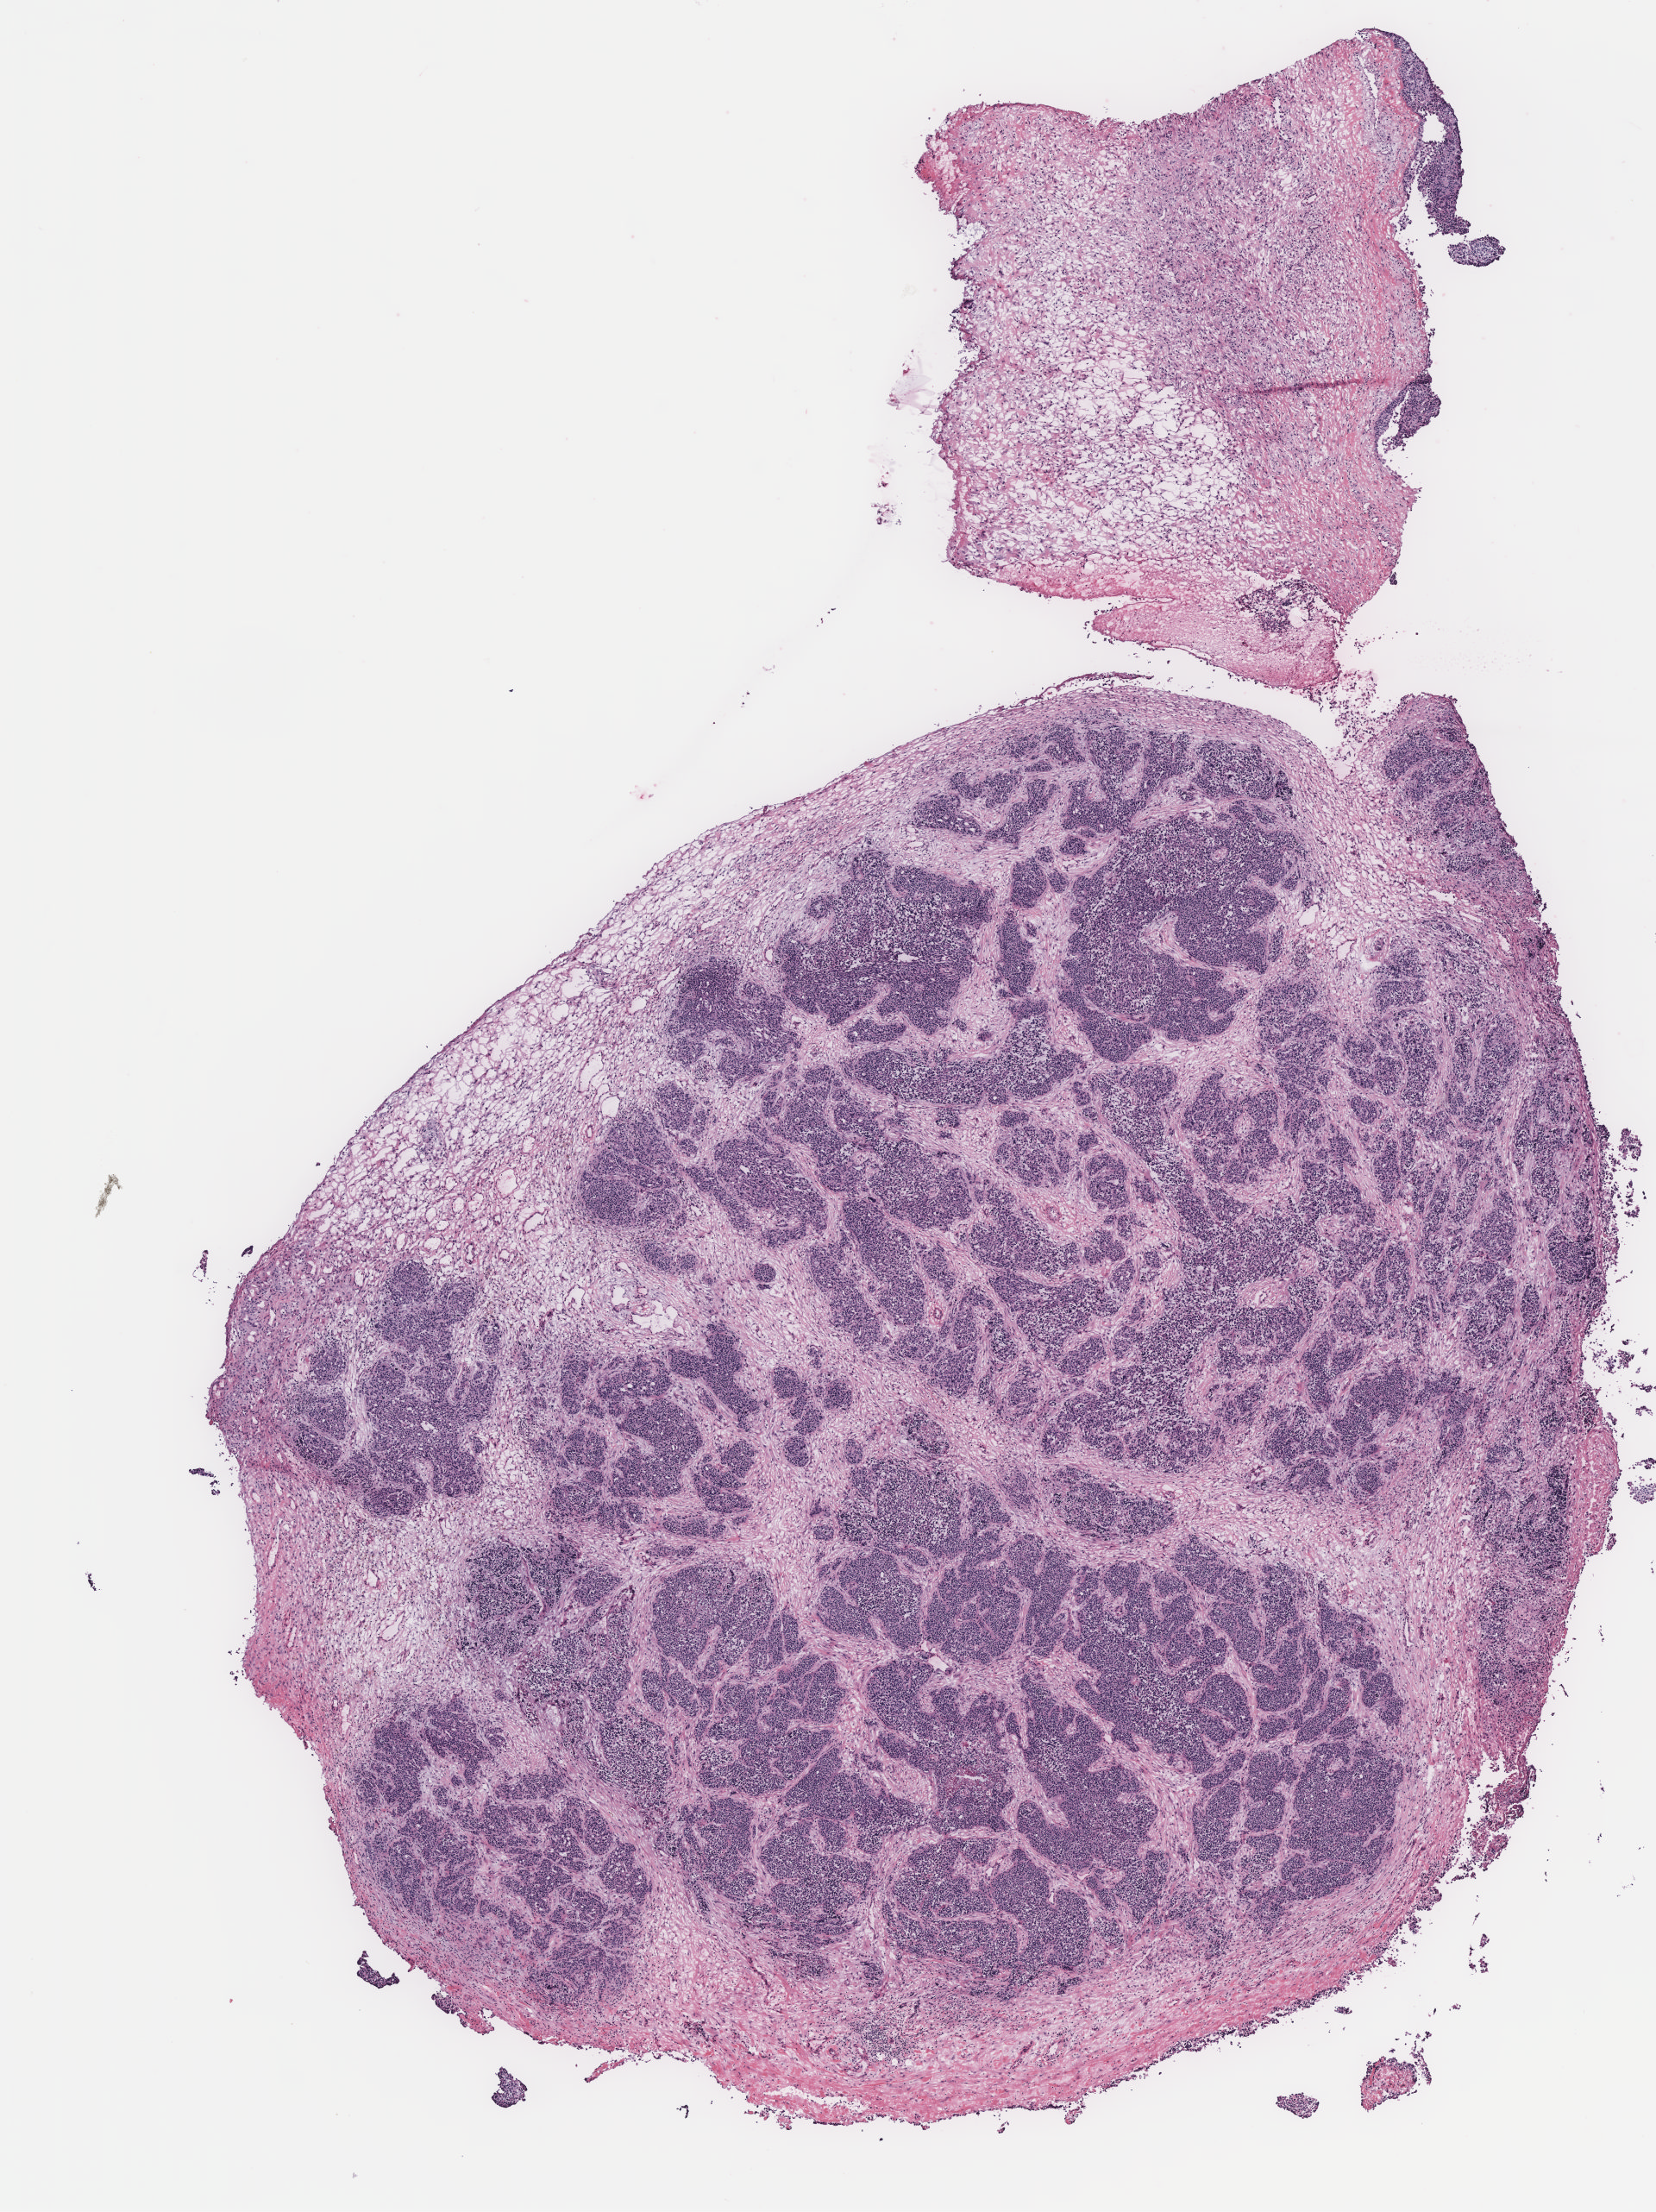
H&E-stained whole-slide image, a low-resolution overview of the entire scanned area, about 7.7 x 10.3 mm (acquisition: 40x scan); ovary, tissue type not recorded. Female patient.
Patient diagnosis: Serous adenocarcinoma, NOS.